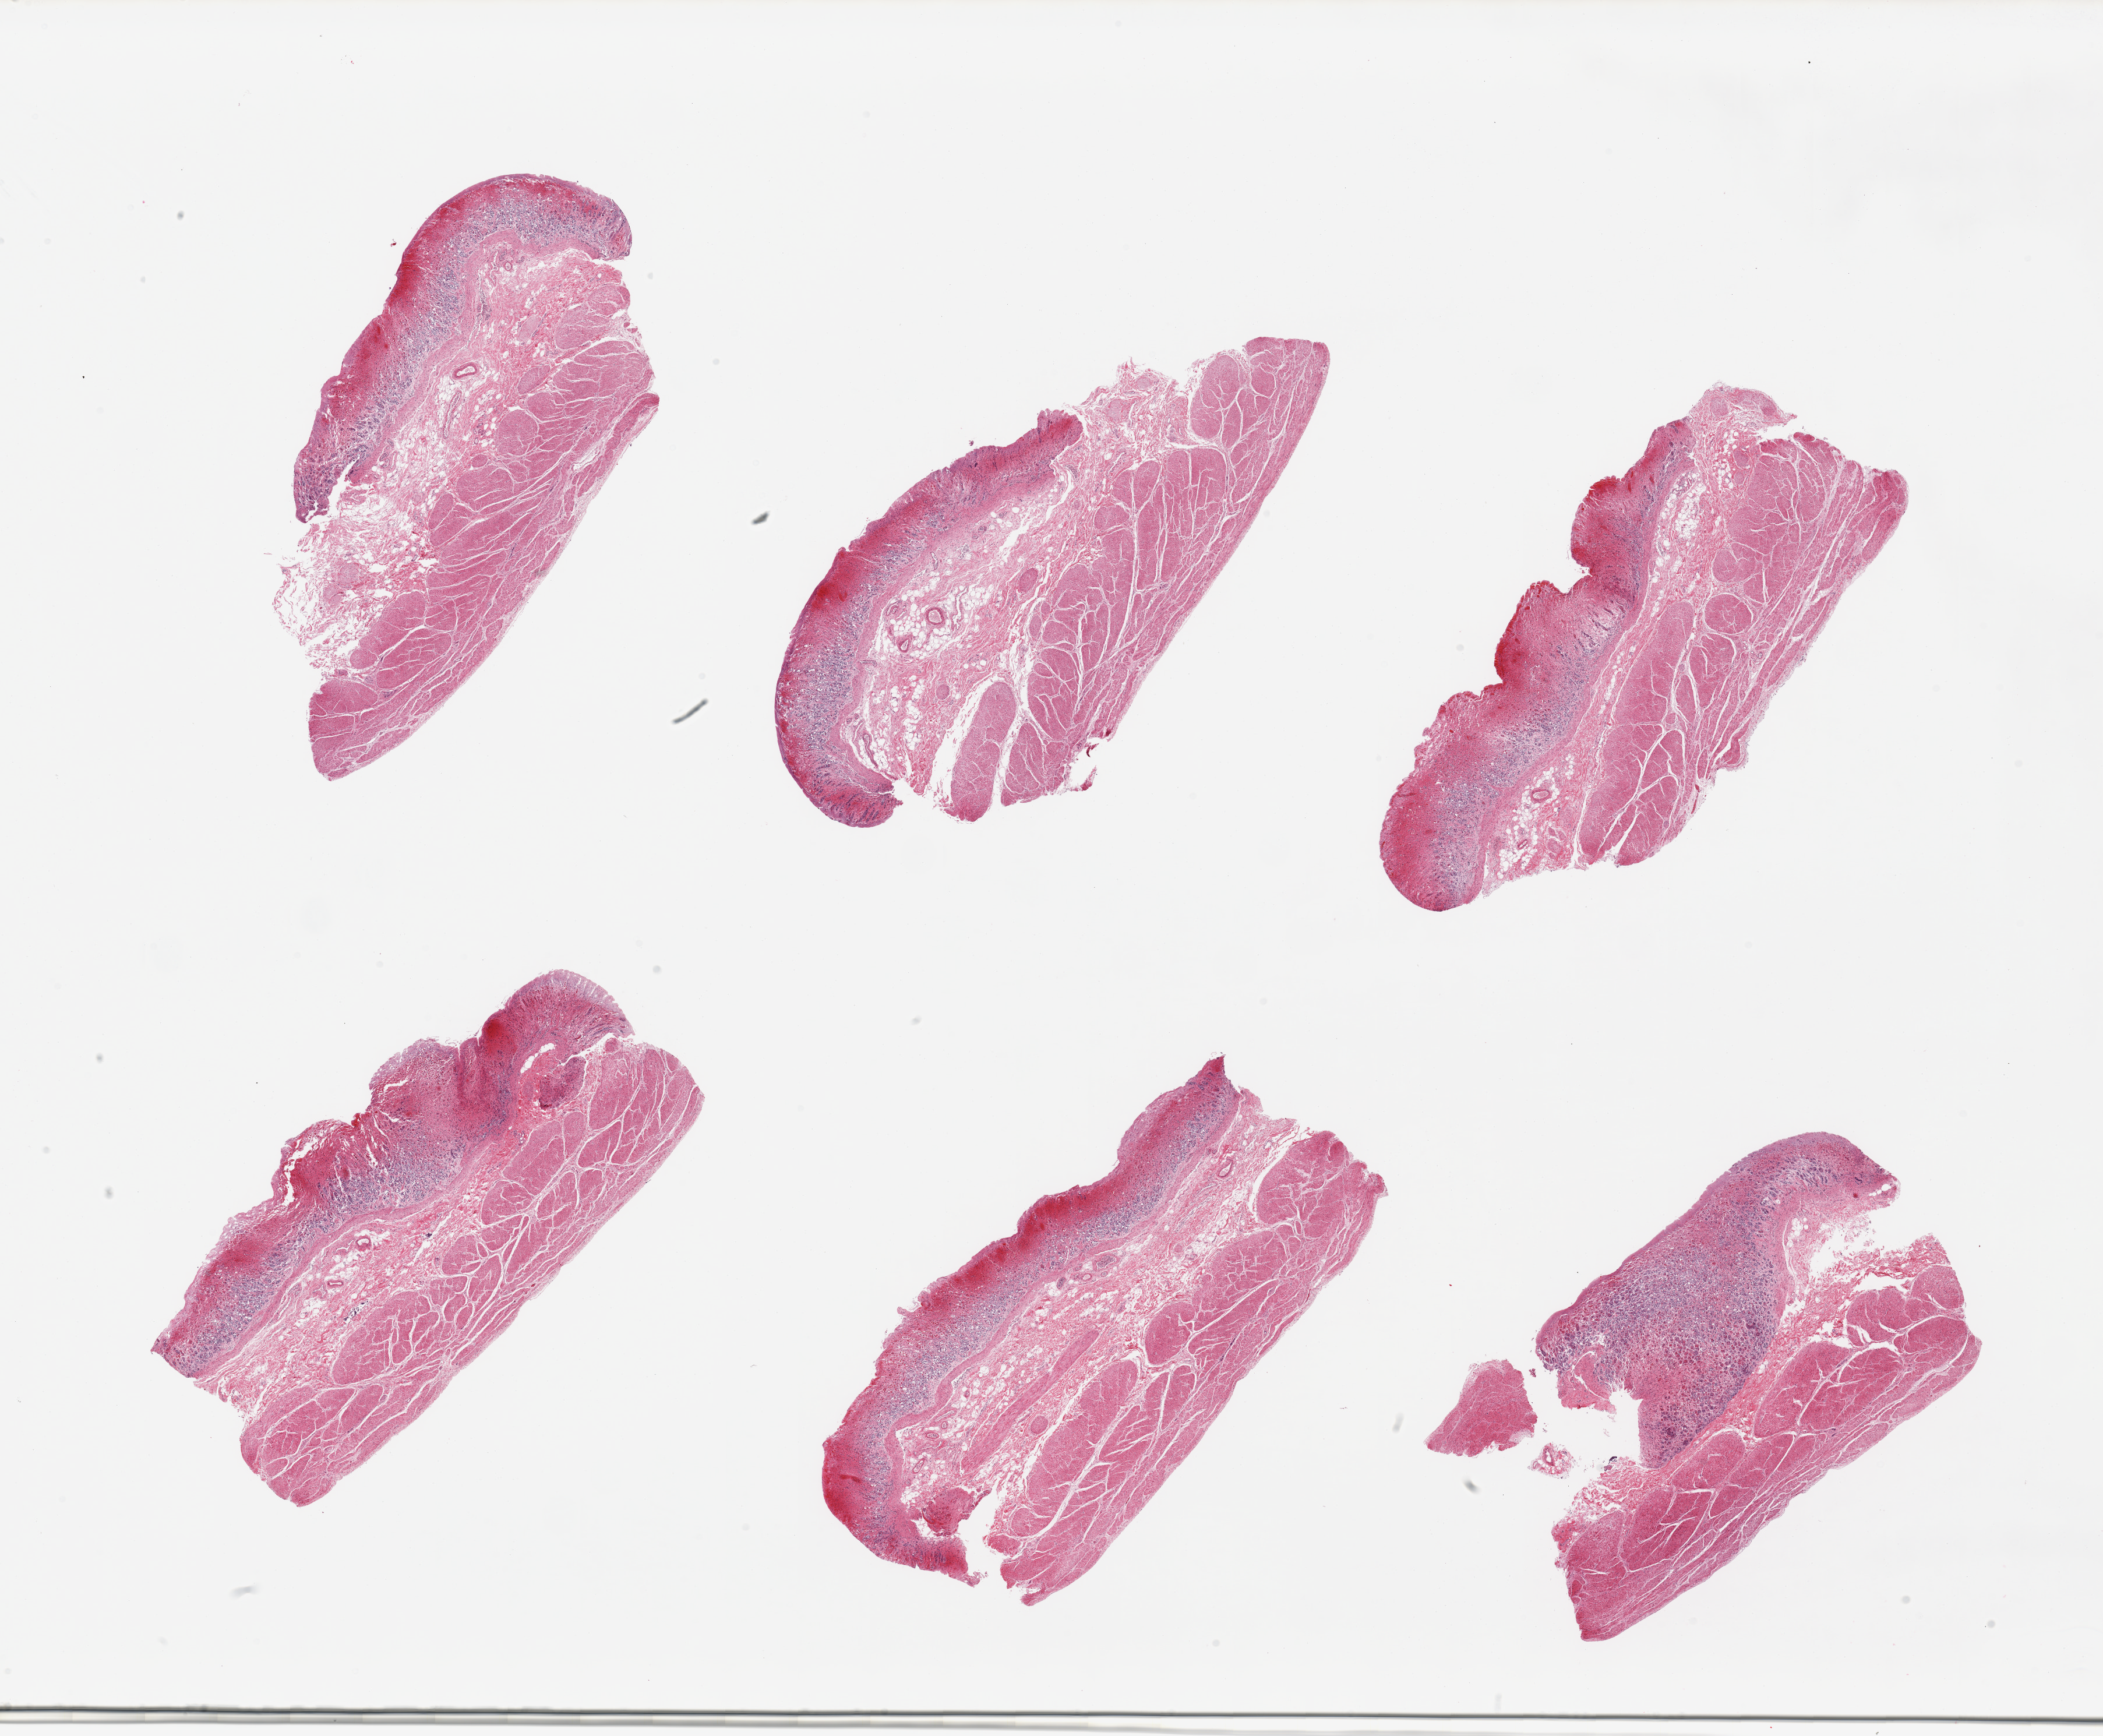
Whole-slide image, H&E stain — shown as a low-resolution overview of the whole scanned area (about 28.5 x 23.6 mm); PAXgene-fixed paraffin-embedded (PFPE) section; target tissue: stomach; tissue donor sample.
* reviewer comment on this tissue sample: 6 pieces, mucosa with advanced autolysis